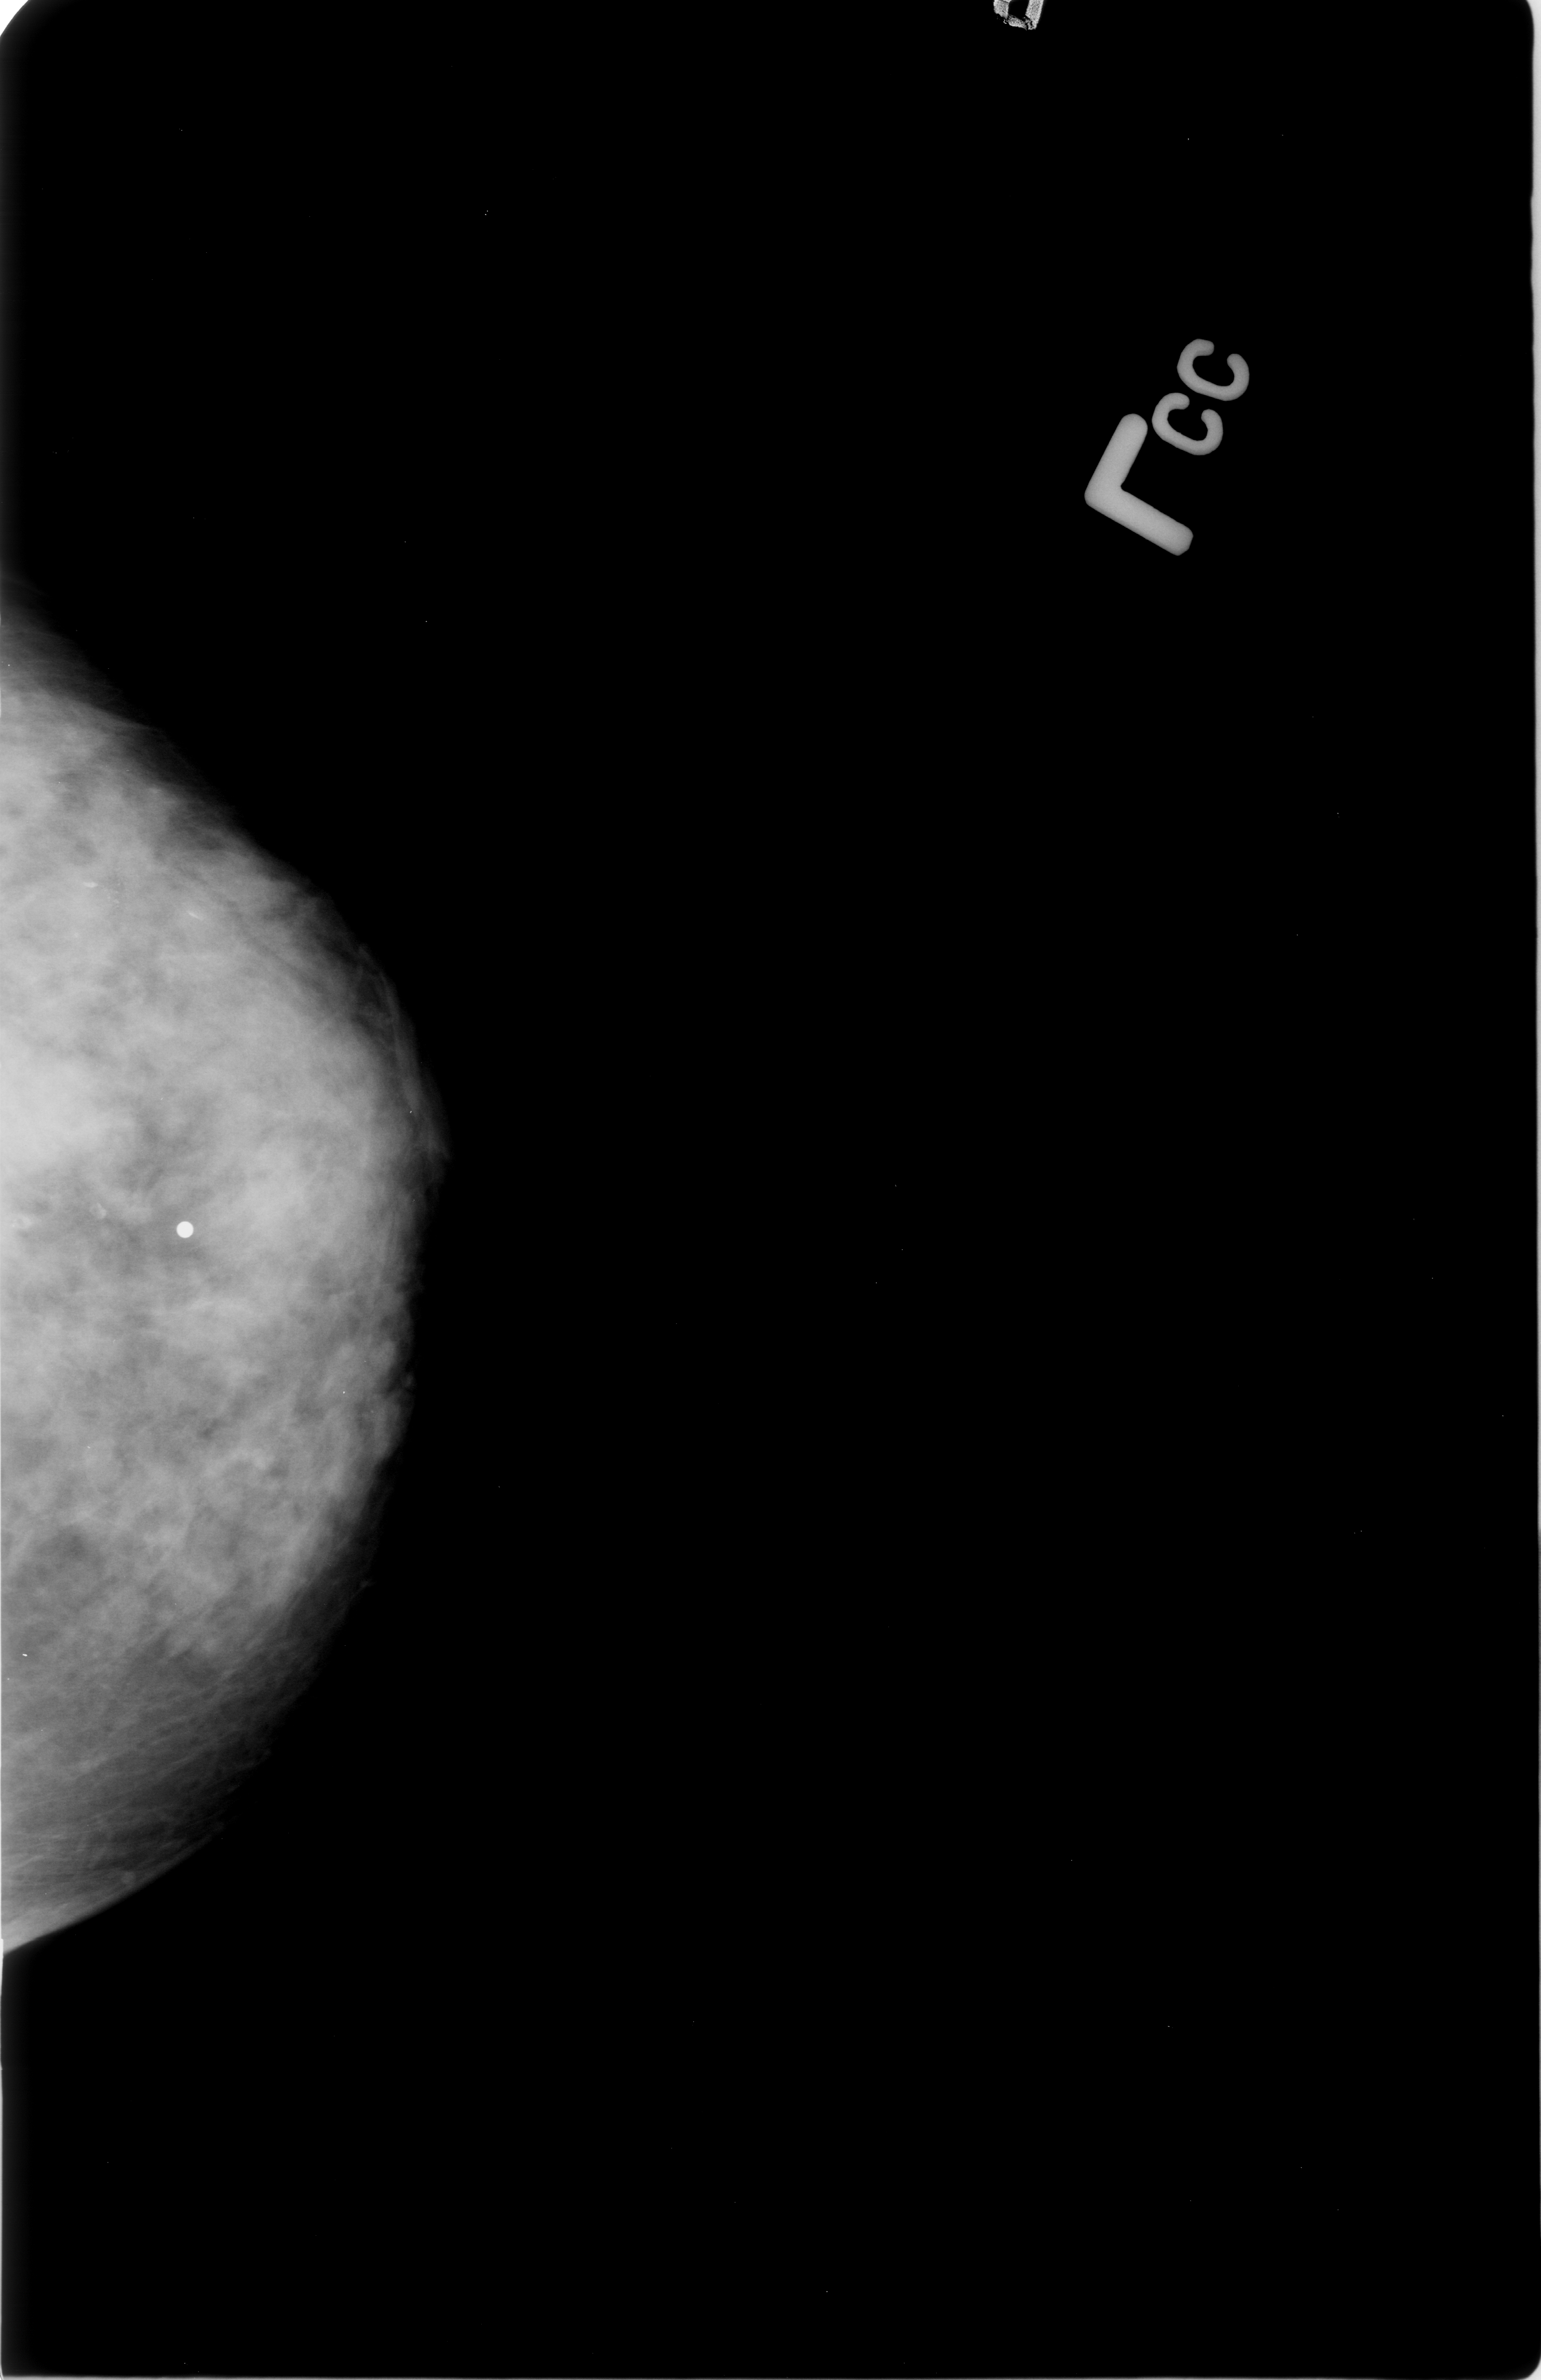
Digitized screen-film mammogram. Left breast. Craniocaudal (CC) view. Breast composition: heterogeneously dense (BI-RADS density category 3 of 4). 1541 × 2380 image matrix.
Expert-marked regions of interest on this image (one box per marked abnormality):
- calcifications, morphology pleomorphic, distribution clustered; BI-RADS assessment category 4; pathology result (as recorded, not read from the image): malignant: box from (x=83, y=843) to (x=175, y=948) px